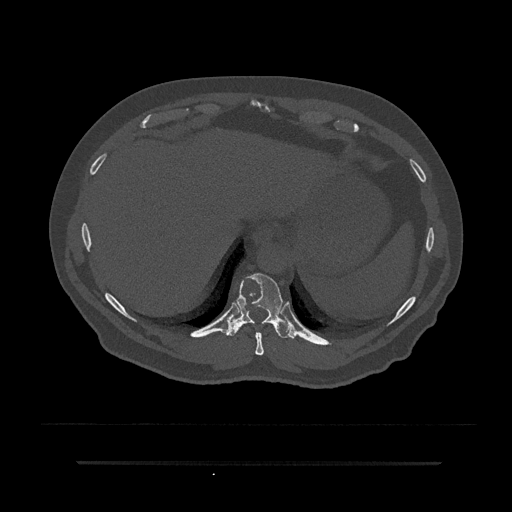
CT including the spine, one axial slice. Slice 343 of 797 in the series (ordered by position). Reconstruction kernel Br40s/3. Bone window (W 1800 / L 400 HU). 0.5 mm slice thickness. 512 × 512 image matrix, field of view 464 × 464 mm. Male patient, age 59 years. Case-level facts recorded for this patient, not image findings: primary cancer: bile ducts; vertebrae with lytic lesions (as recorded): T10.
Annotated regions visible in this slice (semi-automatic segmentation, software-assisted and operator-edited):
- T10 vertebra: box from (x=226, y=273) to (x=294, y=339) px
- T9 vertebra: (x=255, y=332)–(x=264, y=356)